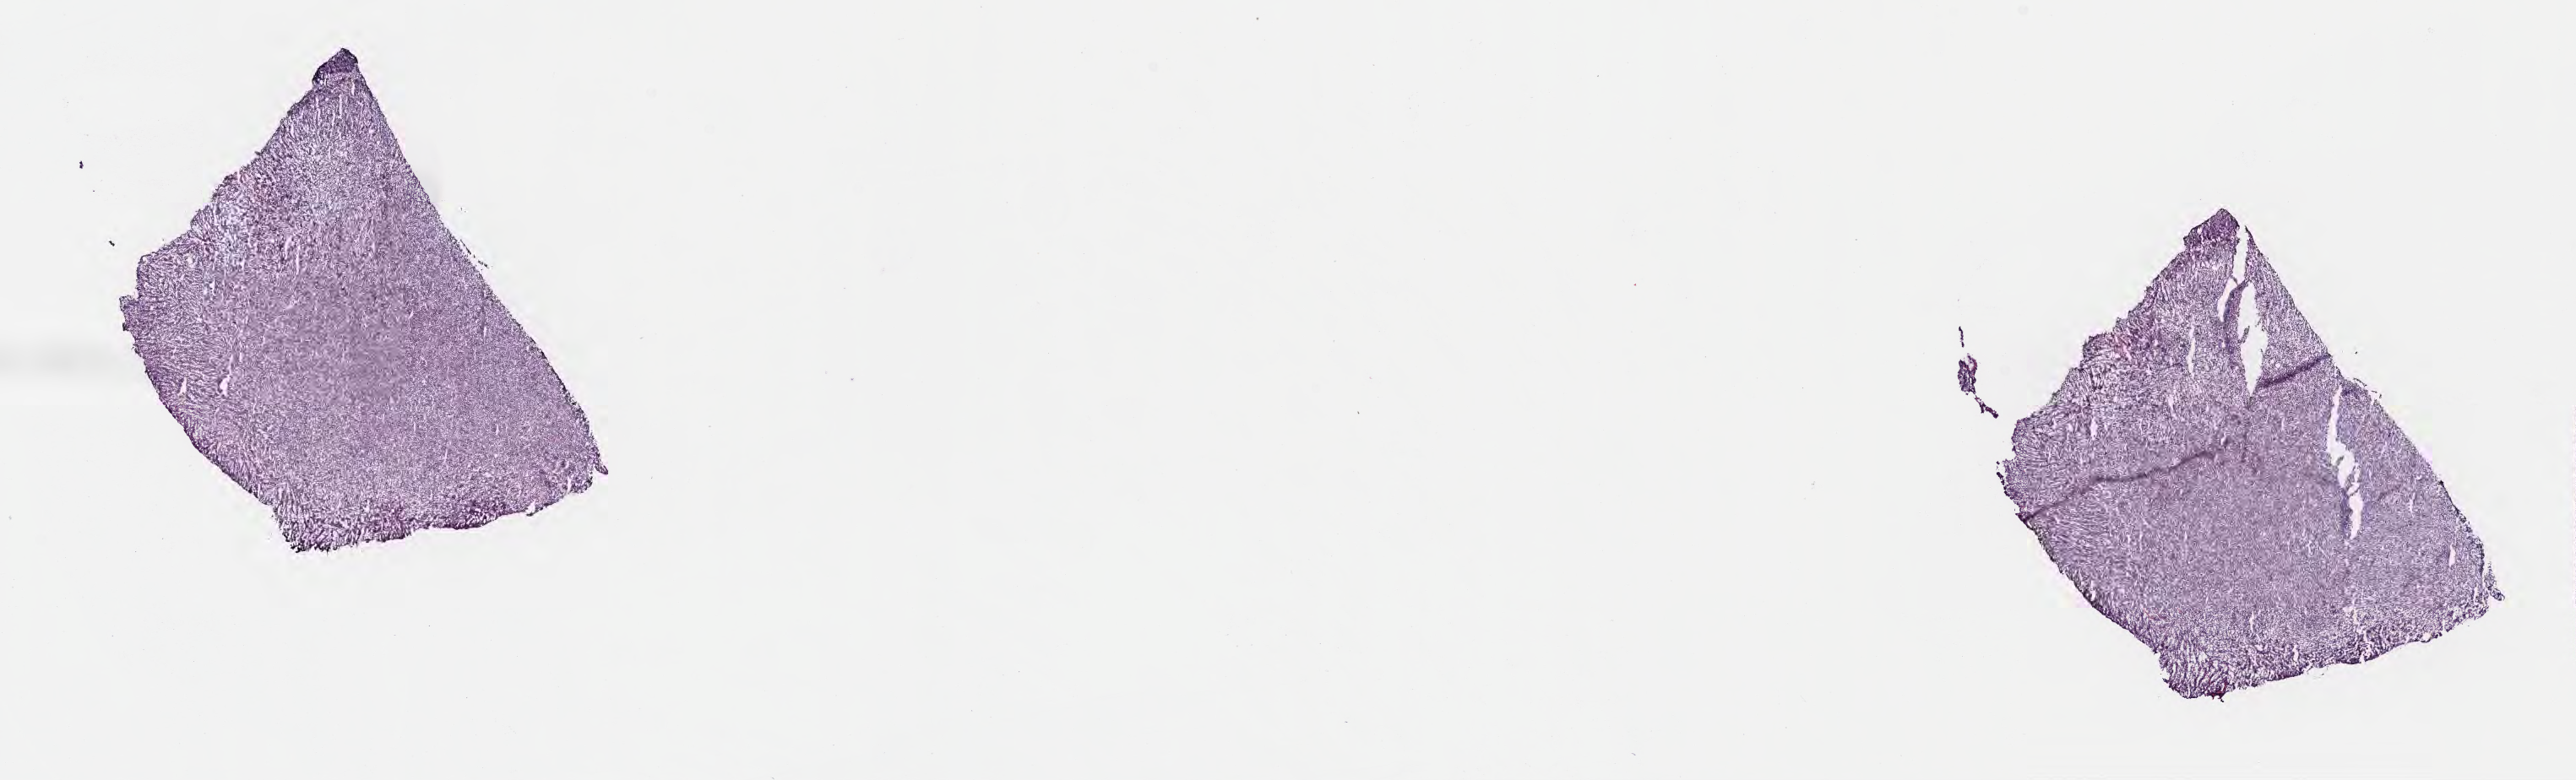
Digitized H&E-stained section, a low-resolution overview of the entire scanned area, about 24.7 x 7.5 mm. Frozen section. Specimen: primary tumor. Anatomic site: cranium. Male, age 8 years at initial diagnosis. Slide review estimates, as recorded: tumor cells 90%, tumor nuclei 90%, stromal cells 5%, necrosis 5%, normal cells 0%. Infiltration values recorded for this section: lymphocyte infiltration 50%, monocyte infiltration 25%, neutrophil infiltration 5%.
Section: bottom of the tissue portion. Diagnosis: Burkitt lymphoma, NOS. Ann Arbor stage (patient): Stage I.